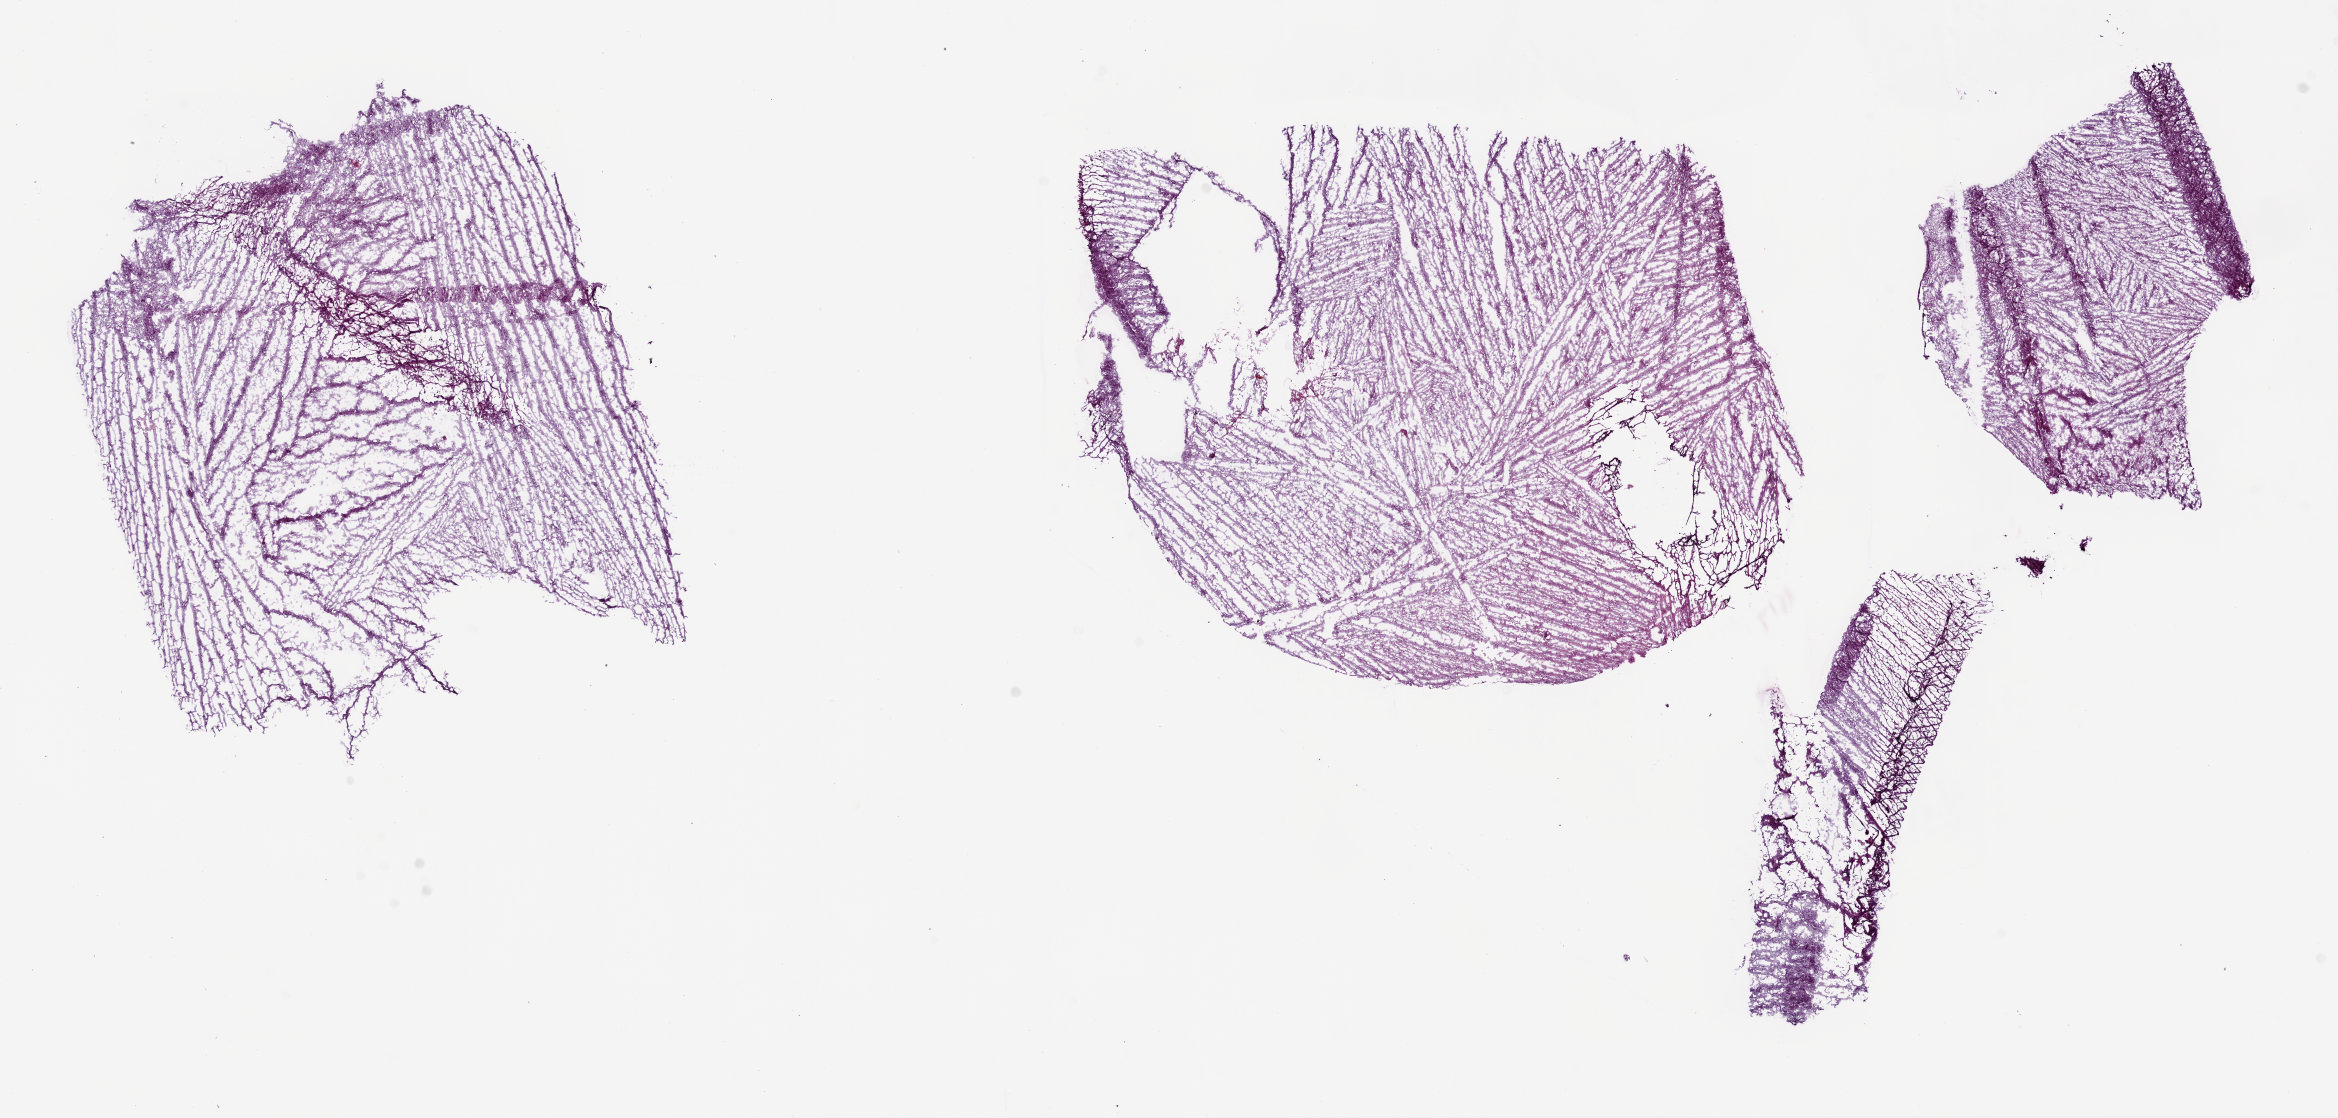
Whole-slide histology image, H&E — shown as a low-resolution overview of the whole scanned area (about 18.7 x 9.0 mm, from a 5x scan); frozen section from the bottom of the tissue portion; sample: primary tumour, brain. Male patient; age at initial diagnosis 43 years. Histologic grade: G2 (moderately differentiated). Pathologist review of this section (percent, as recorded): tumour cells 100%, tumour nuclei 75%, normal cells 0%, stromal cells 0%, necrosis 0%.
Histologic diagnosis: Mixed glioma.